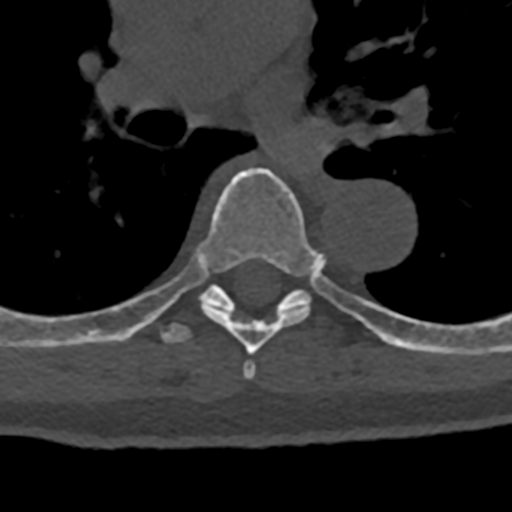
CT including the spine, one axial slice. Position 797 of 797 along the scan axis. Reconstruction kernel Br40s/3. Bone window (W 1800 / L 400 HU). 0.5 mm slice thickness. 512 × 512 image matrix, field of view 160 × 160 mm. Male patient, age 74 years. Case-level facts recorded for this patient, not image findings: primary cancer: renal; vertebrae with lytic lesions (as recorded): T10, L1, L2, L3, L4, L5.
Structures marked on this image (semi-automatic segmentation, software-assisted and operator-edited):
- T6 vertebra: bounding box [x1, y1, x2, y2] px = [143, 168, 318, 379]
- T7 vertebra: [70, 253, 431, 352]